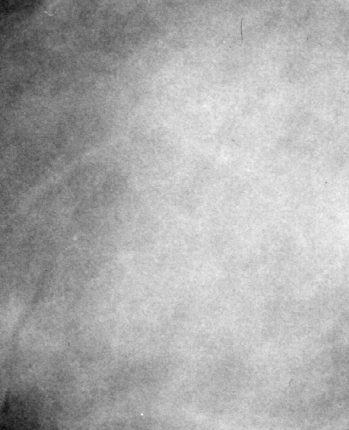
Crop from a digitized film mammogram around one marked abnormality; right breast; CC view.
- Finding: mass, shape round, margins circumscribed / obscured; BI-RADS assessment category 3; subtlety rating 2 on a 1 (subtle) to 5 (obvious) scale; pathology (as recorded): benign.